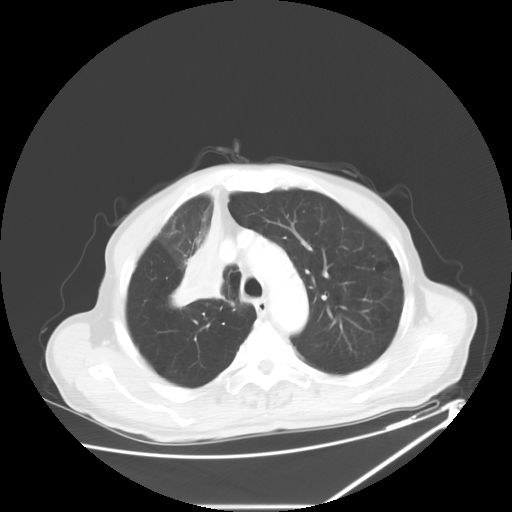
Chest CT, one axial slice. Slice 46 of 60 in the series (ordered by position). Reconstruction kernel STANDARD. Lung window (W 1500 / L -600 HU). 512 × 512 image matrix, field of view 410 × 410 mm. Patient: male, 73 years. From the clinical record (not read from this slice): clinical TNM (as recorded): T2a N1 M0.
Structures marked on this image (rectangle marked by the reading radiologist):
- lung tumour (recorded histology: squamous cell carcinoma): bounding box [x1, y1, x2, y2] px = [161, 198, 231, 306]